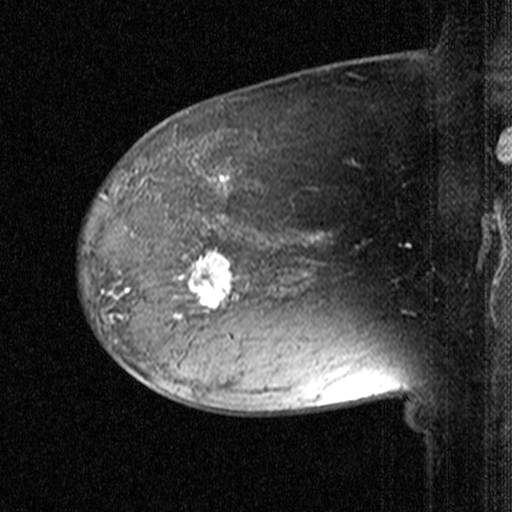
Breast MRI (dynamic contrast-enhanced), one sagittal slice; position 30 of 44 along the scan axis; dynamic contrast-enhanced study with each time point stored as its own series, time point 2 of 3 at this slice position (early post-contrast, ordered by acquisition time); 1.5 T; TE 4.5 ms, TR 11 ms; 3 mm slice thickness; 512 × 512 image matrix. Patient: female, 38 years. Case-level facts recorded for this patient, not image findings: setting: breast cancer imaged before/during neoadjuvant chemotherapy; receptor status: HR-positive, HER2-negative.
Annotated regions visible in this slice (semi-automatic segmentation, software-assisted and operator-edited):
- analysis volume of interest (the breast-tissue region the enhancement analysis was run in; not a lesion): bounding box (x1, y1, x2, y2) in pixels: (170, 232, 259, 331)
- tumour enhancement mask (voxels above the 90 % enhancement threshold inside the analysis volume of interest): (177, 250, 238, 317)